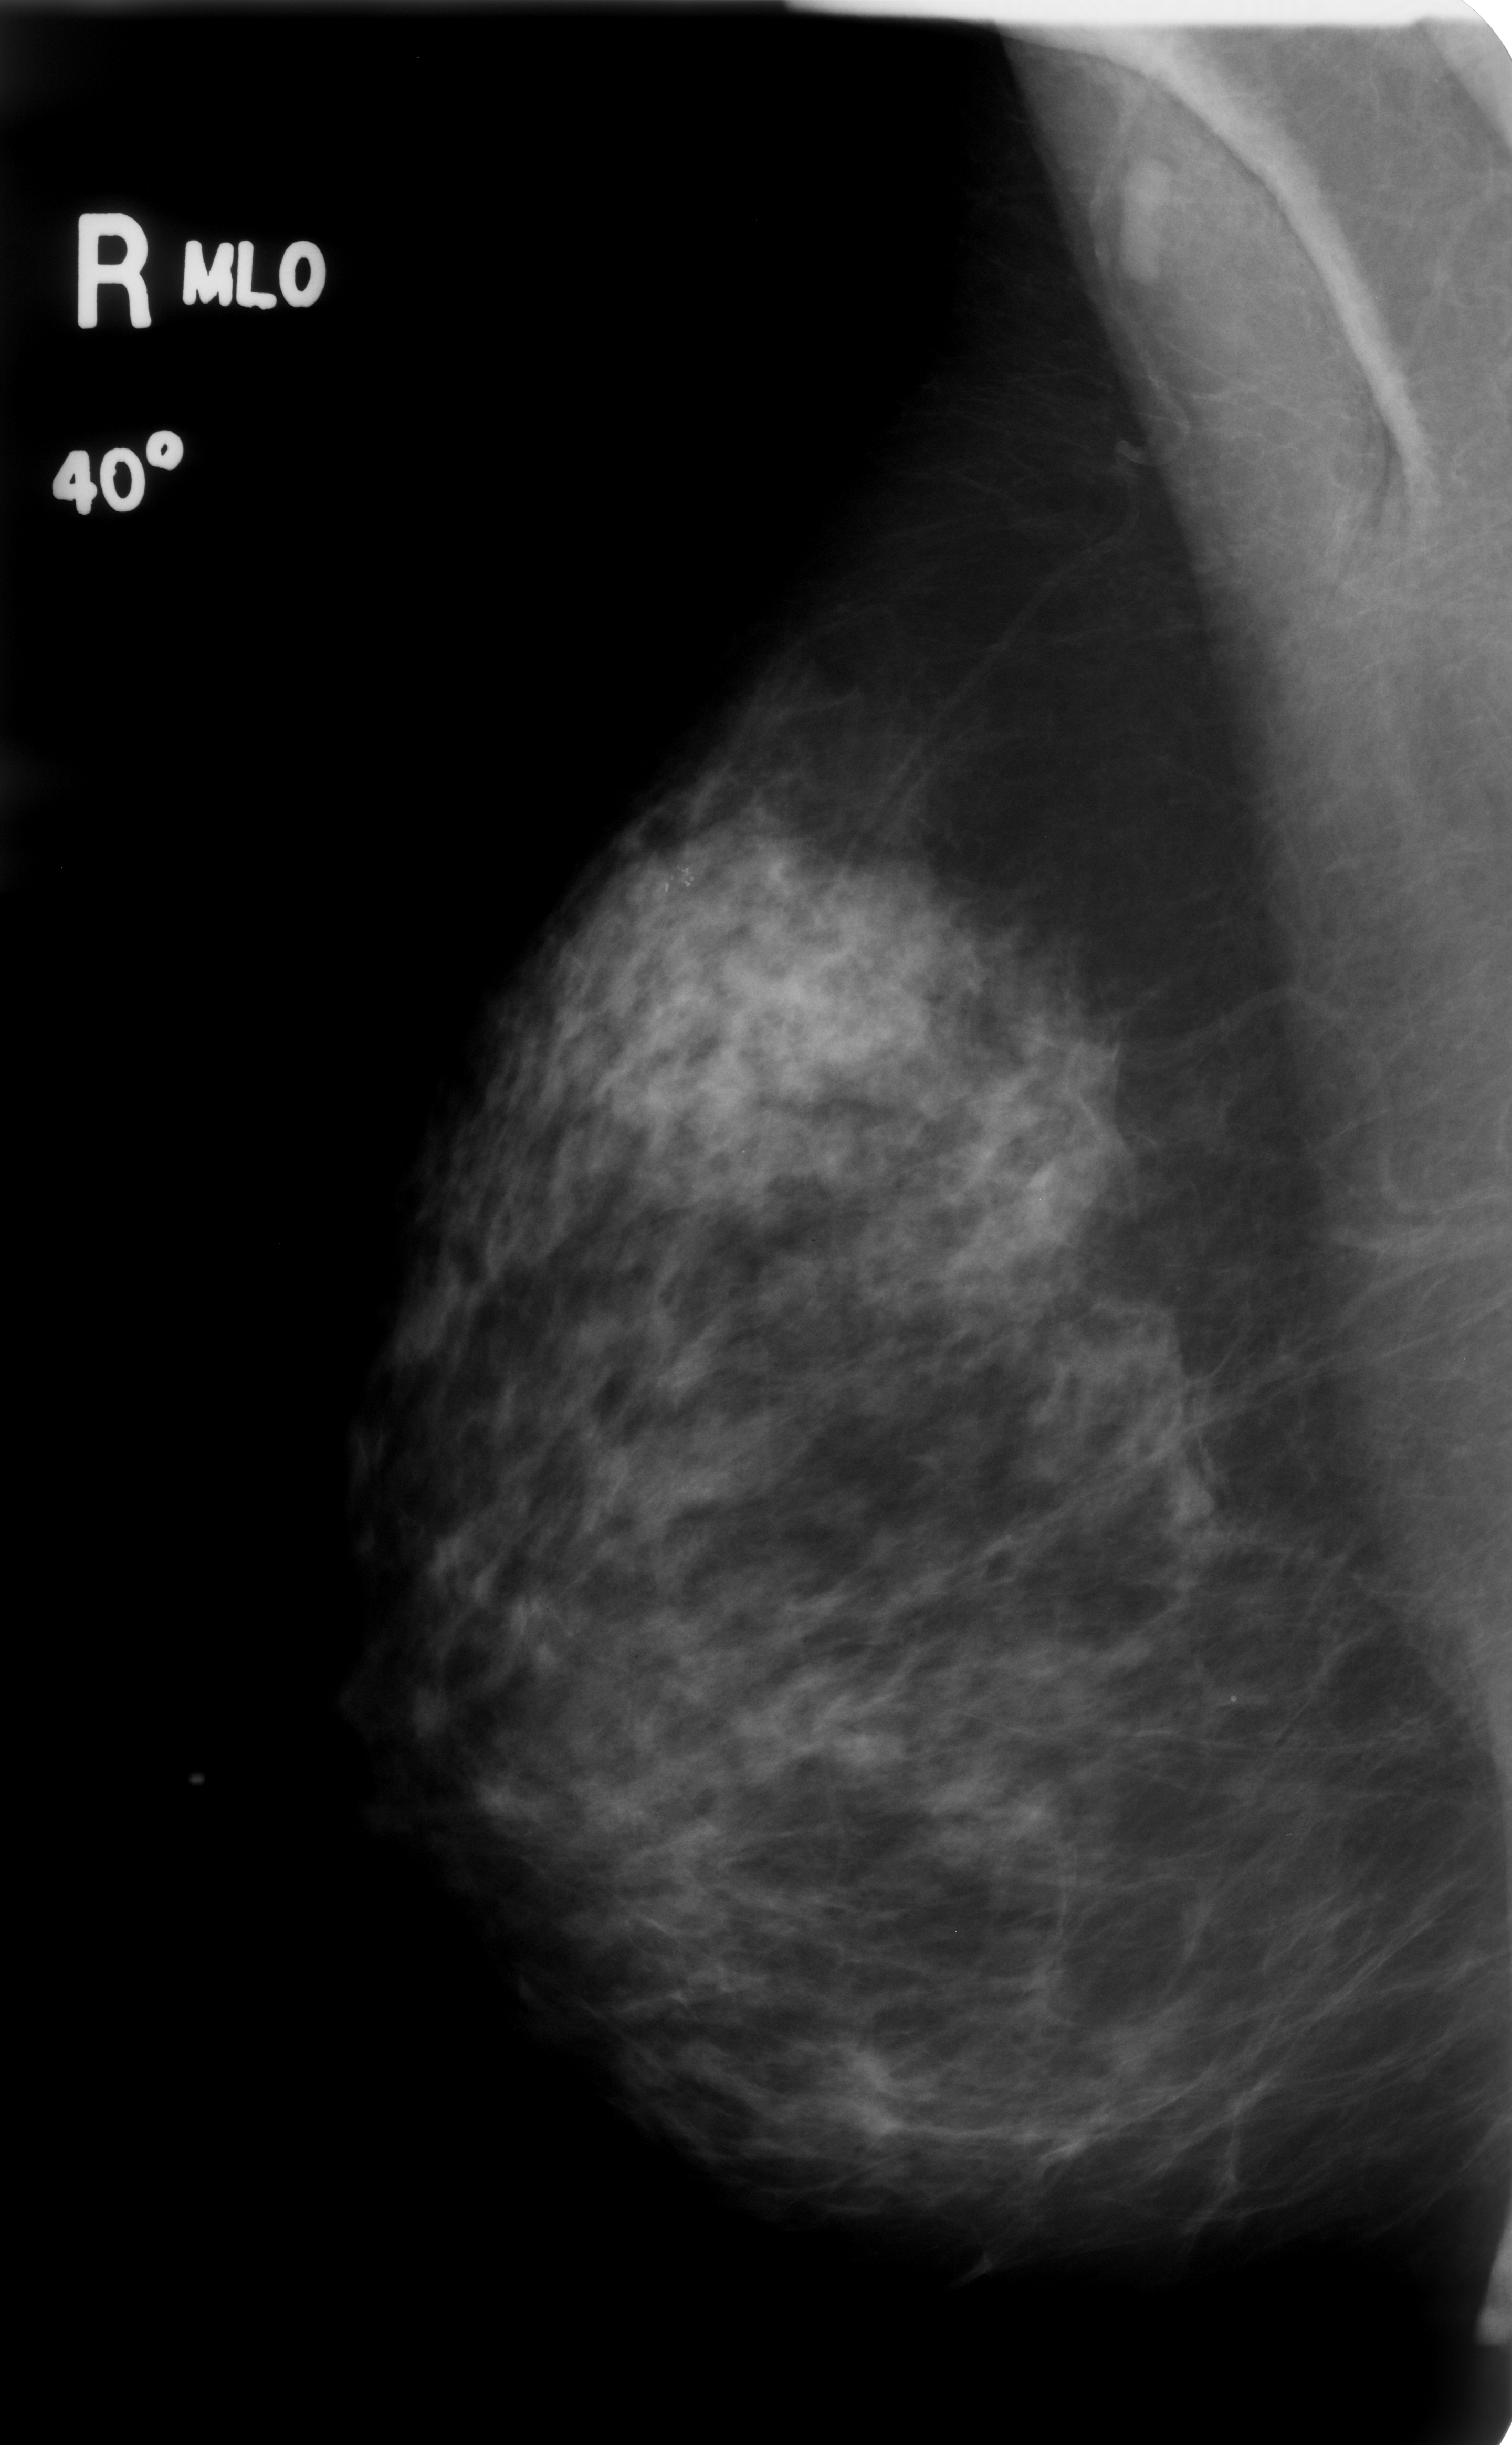
Mammogram (digitized film); right breast; MLO view; breast composition: heterogeneously dense (BI-RADS density category 3 of 4).
- Calcifications, morphology pleomorphic, distribution clustered; BI-RADS assessment category 4; subtlety rating 4 on a 1 (subtle) to 5 (obvious) scale; pathology (as recorded): benign.